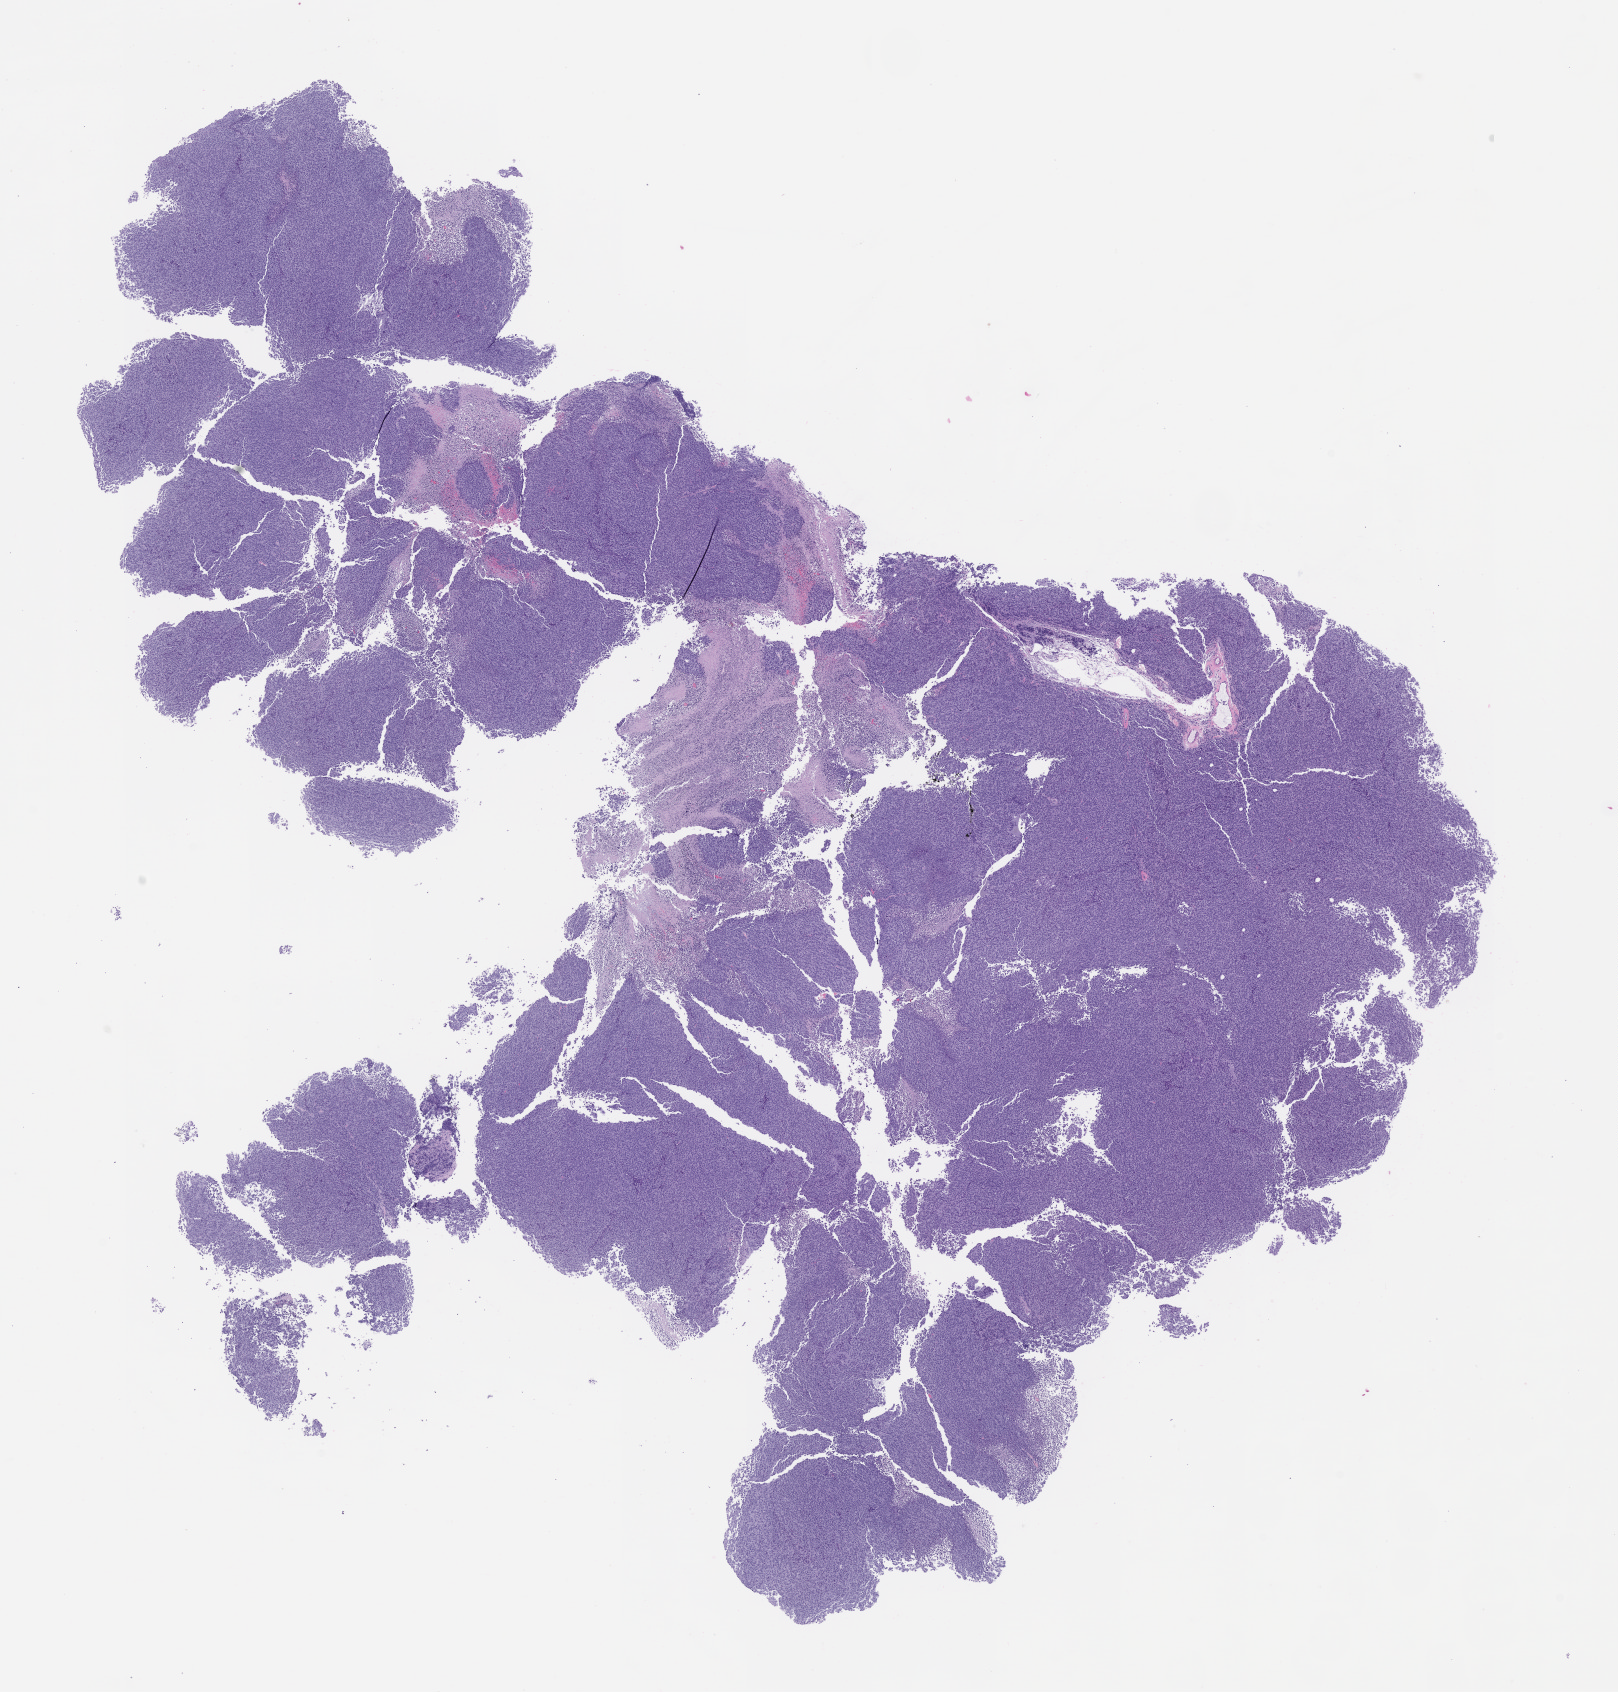
Whole-slide image, hematoxylin and eosin (H&E): patient-derived xenograft (human tumor grown in a mouse), passage 2, shown as a low-resolution overview of the whole scanned area (about 13.0 x 13.6 mm). Formalin-fixed paraffin-embedded section. Tumor site category: musculoskeletal.
Originating patient diagnosis: Ewing Sarcoma|Primitive Neuroectodermal Tumor.